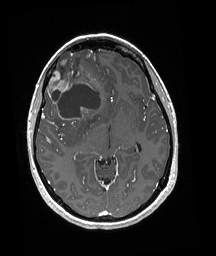
Brain MRI from a brain-tumour surgery series, one axial slice; position 107 of 192 along the scan axis; T1-weighted post-contrast; 1 mm slice thickness; 216 × 256 image matrix. From the clinical record (not read from this slice): histopathology: Oligodendroglioma; WHO grade: 3; IDH mutation: yes; tumour location: Right Frontal.
Outlined on this slice (expert manual segmentation):
- tumour: bounding box (x1, y1, x2, y2) in pixels: (48, 51, 101, 124)